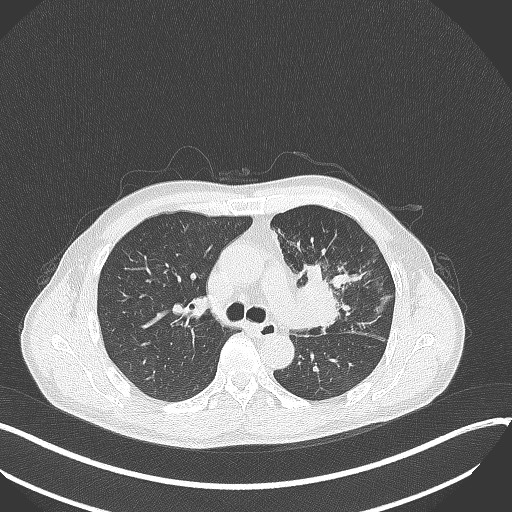
Chest CT, one axial slice. Position 219 of 411 along the scan axis. 120 kVp. Lung window (W 1500 / L -600 HU). 1 mm slice thickness. 512 × 512 image matrix, field of view 400 × 400 mm. Patient: male, 56 years. From the clinical record (not read from this slice): clinical TNM (as recorded): T2a N0 M0.
Structures marked on this image (rectangle marked by the reading radiologist):
- lung tumour (recorded histology: squamous cell carcinoma): box from (x=290, y=263) to (x=348, y=338) px